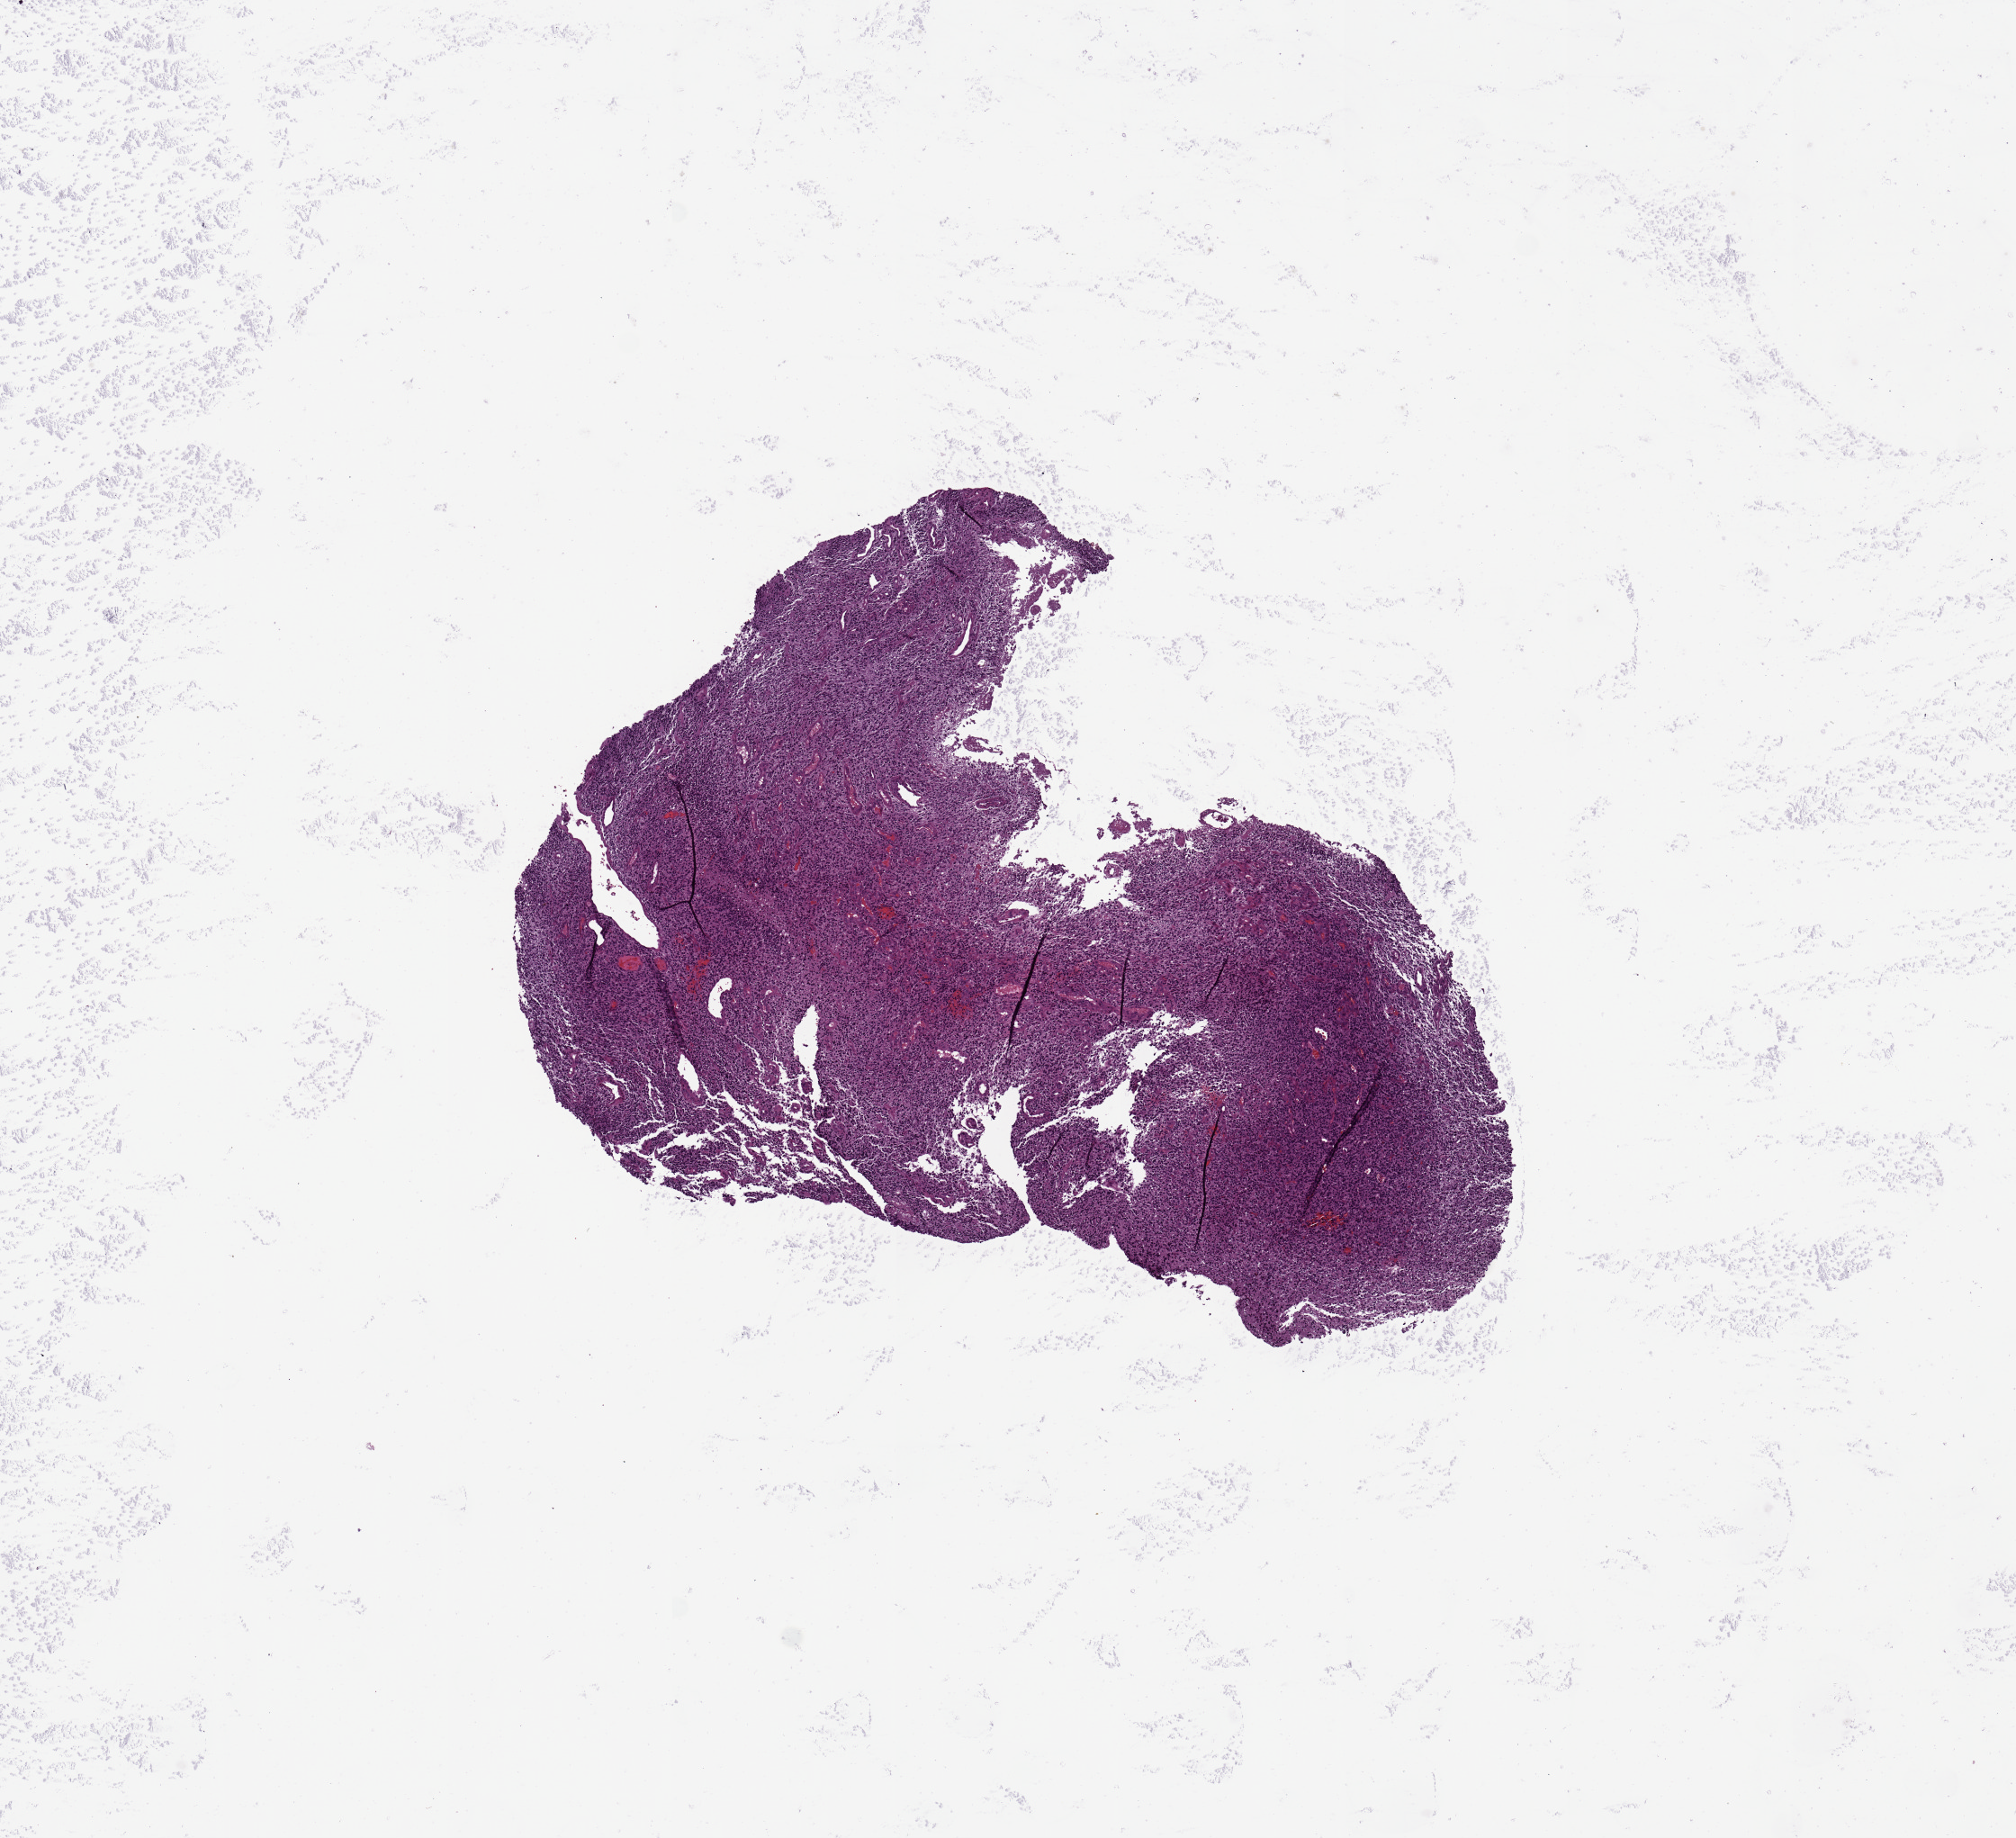
Digitized H&E-stained tissue section (whole slide) — low-resolution overview of the scanned area, about 8.9 x 8.1 mm, tumour tissue sample, brain. 35-year-old male patient.
- histologic diagnosis: Glioblastoma